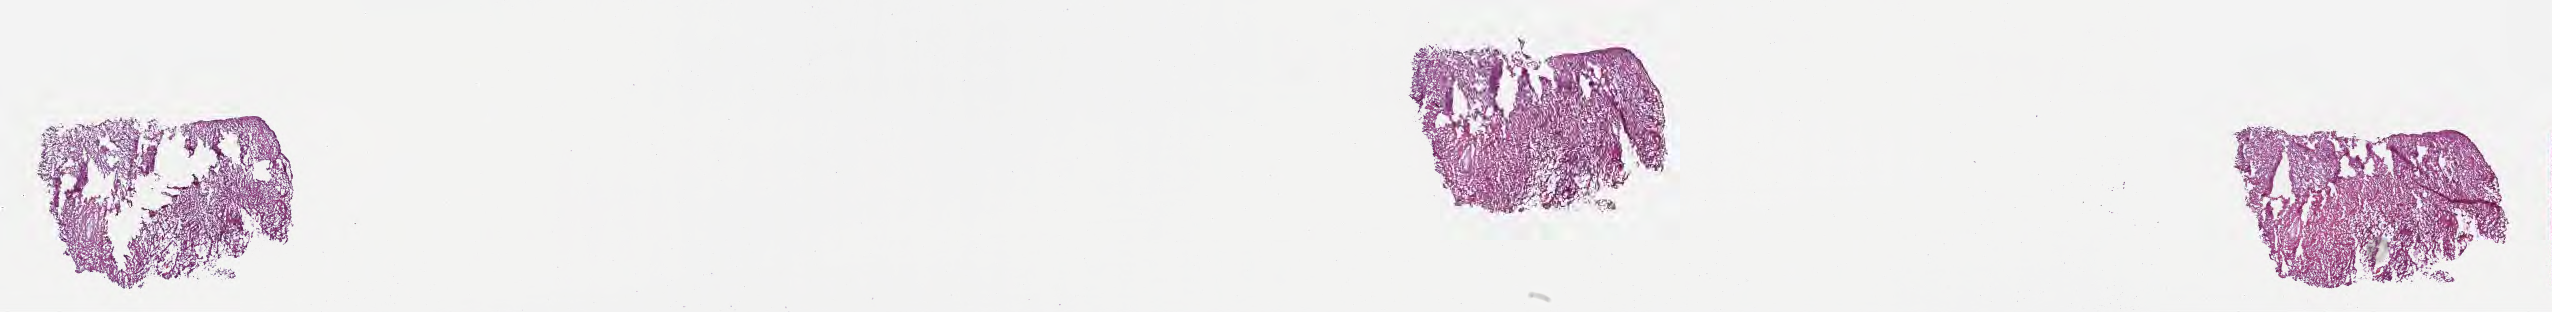
Digitized haematoxylin and eosin-stained section of tumor tissue from the brain — low-resolution overview of the scanned area, about 41.3 x 5.0 mm. Frozen section. Patient: female, age 69 months (5 years 9 months).
Diagnosis: Meningioma, NOS.